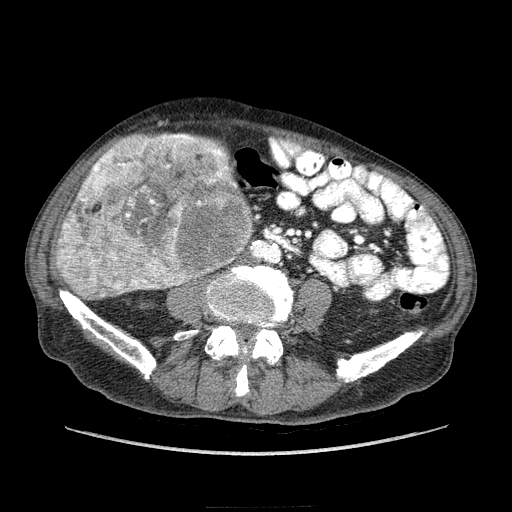
Contrast-enhanced abdominal CT (liver protocol), one axial slice; slice 47 of 218 in the series (ordered by position); 100 kVp; soft-tissue window (W 400 / L 40 HU); 2.5 mm slice thickness; 512 × 512 image matrix, field of view 380 × 380 mm. From the clinical record (not read from this slice): diagnosis: hepatocellular carcinoma (patient treated with transarterial chemoembolisation; whether this scan precedes or follows treatment is not stated here); TNM stage (as recorded): Stage-IIIA; Child-Pugh class: A; tumour differentiation: well differentiated.
Structures marked on this image (semi-automatic segmentation, software-assisted and operator-edited):
- liver parenchyma outside the tumour (the mass and vessels are separate outlines, so this box may not span the whole liver): bounding box [x1, y1, x2, y2] px = [56, 160, 252, 290]
- mass: [57, 132, 253, 300]